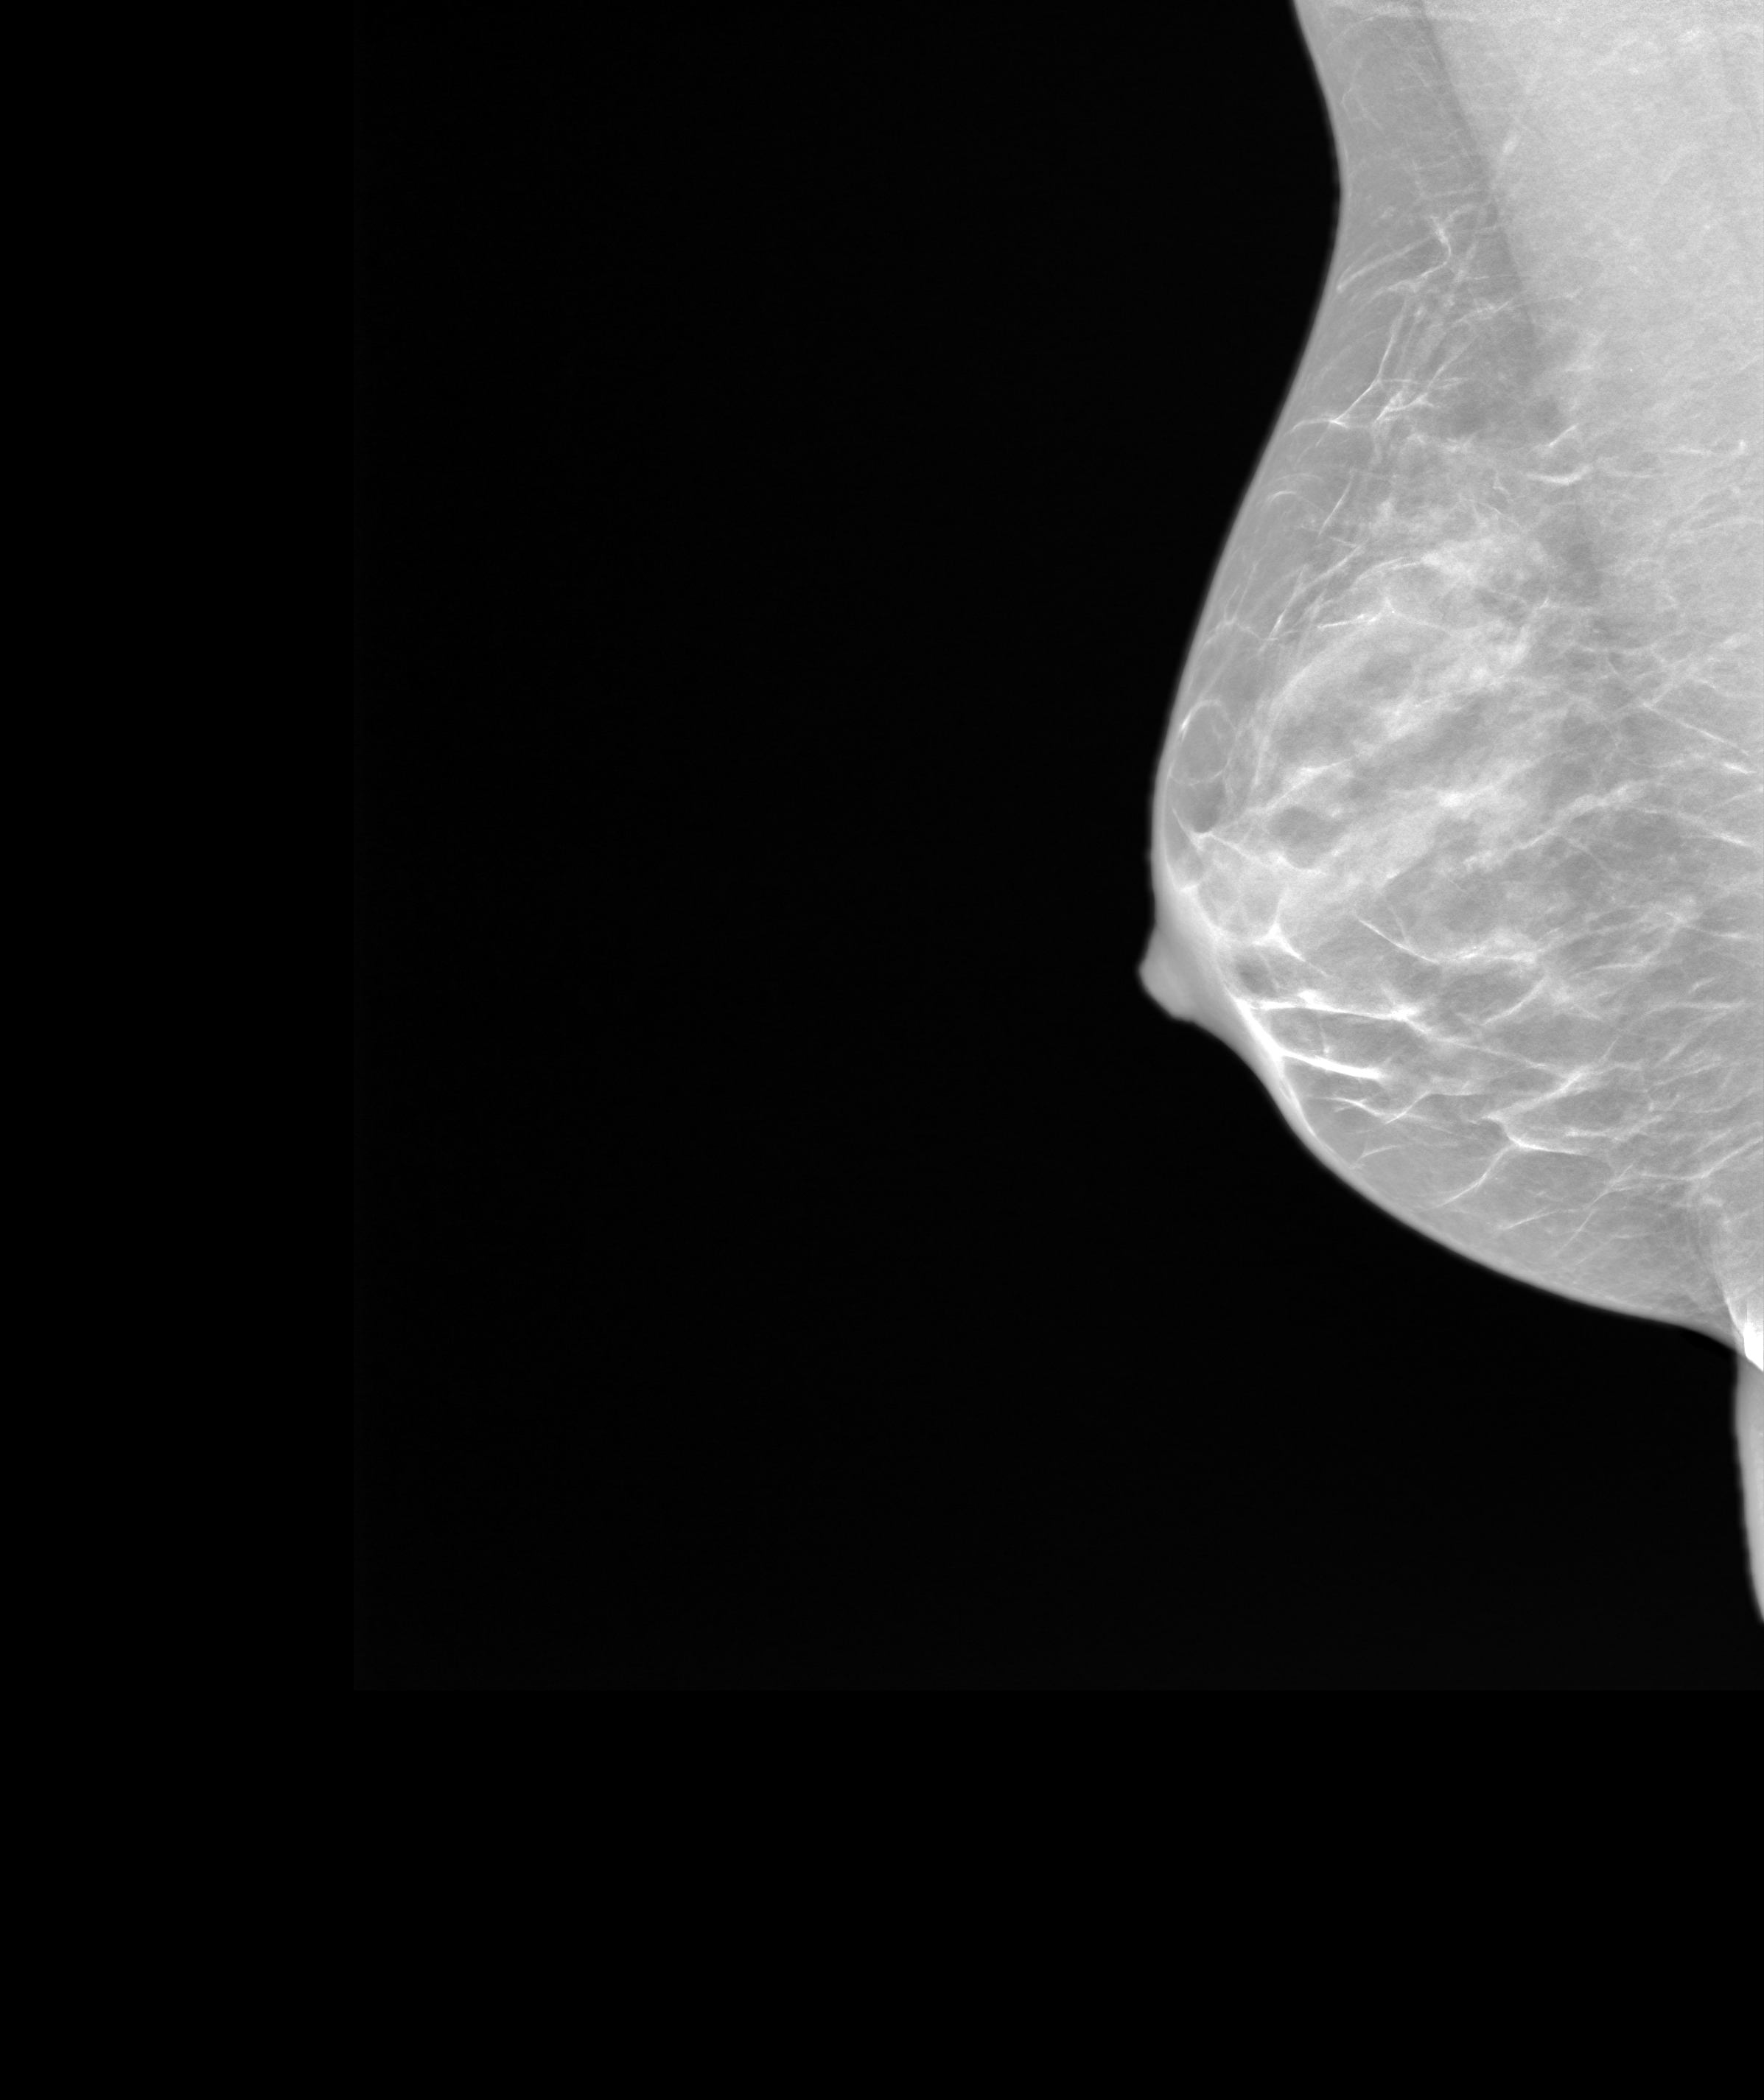
Annual screening mammography examination. Patient aged 49 years (female).
Image type: synthesized 2-D view from tomosynthesis. Breast: right. Projection: MLO view.